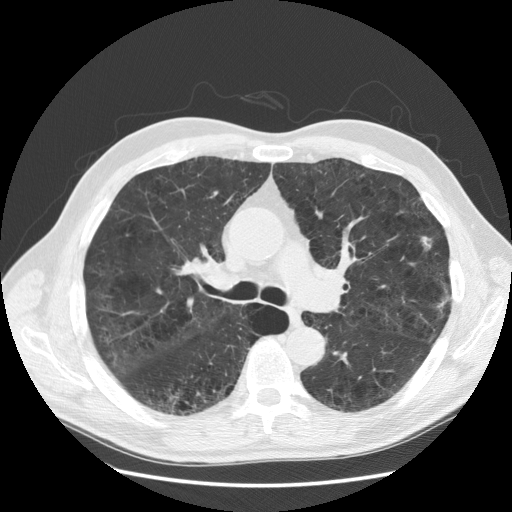
Low-dose screening chest CT, one axial slice; slice 96 of 163 in the series (ordered by position); 120 kVp; lung window (W 1500 / L -600 HU); 2.5 mm slice thickness; 512 × 512 image matrix, field of view 380 × 380 mm.
Outlined on this slice (outlined manually by an expert reader):
- lesion 1 (tumor, upper lobe of left lung): box from (x=420, y=236) to (x=432, y=251) px